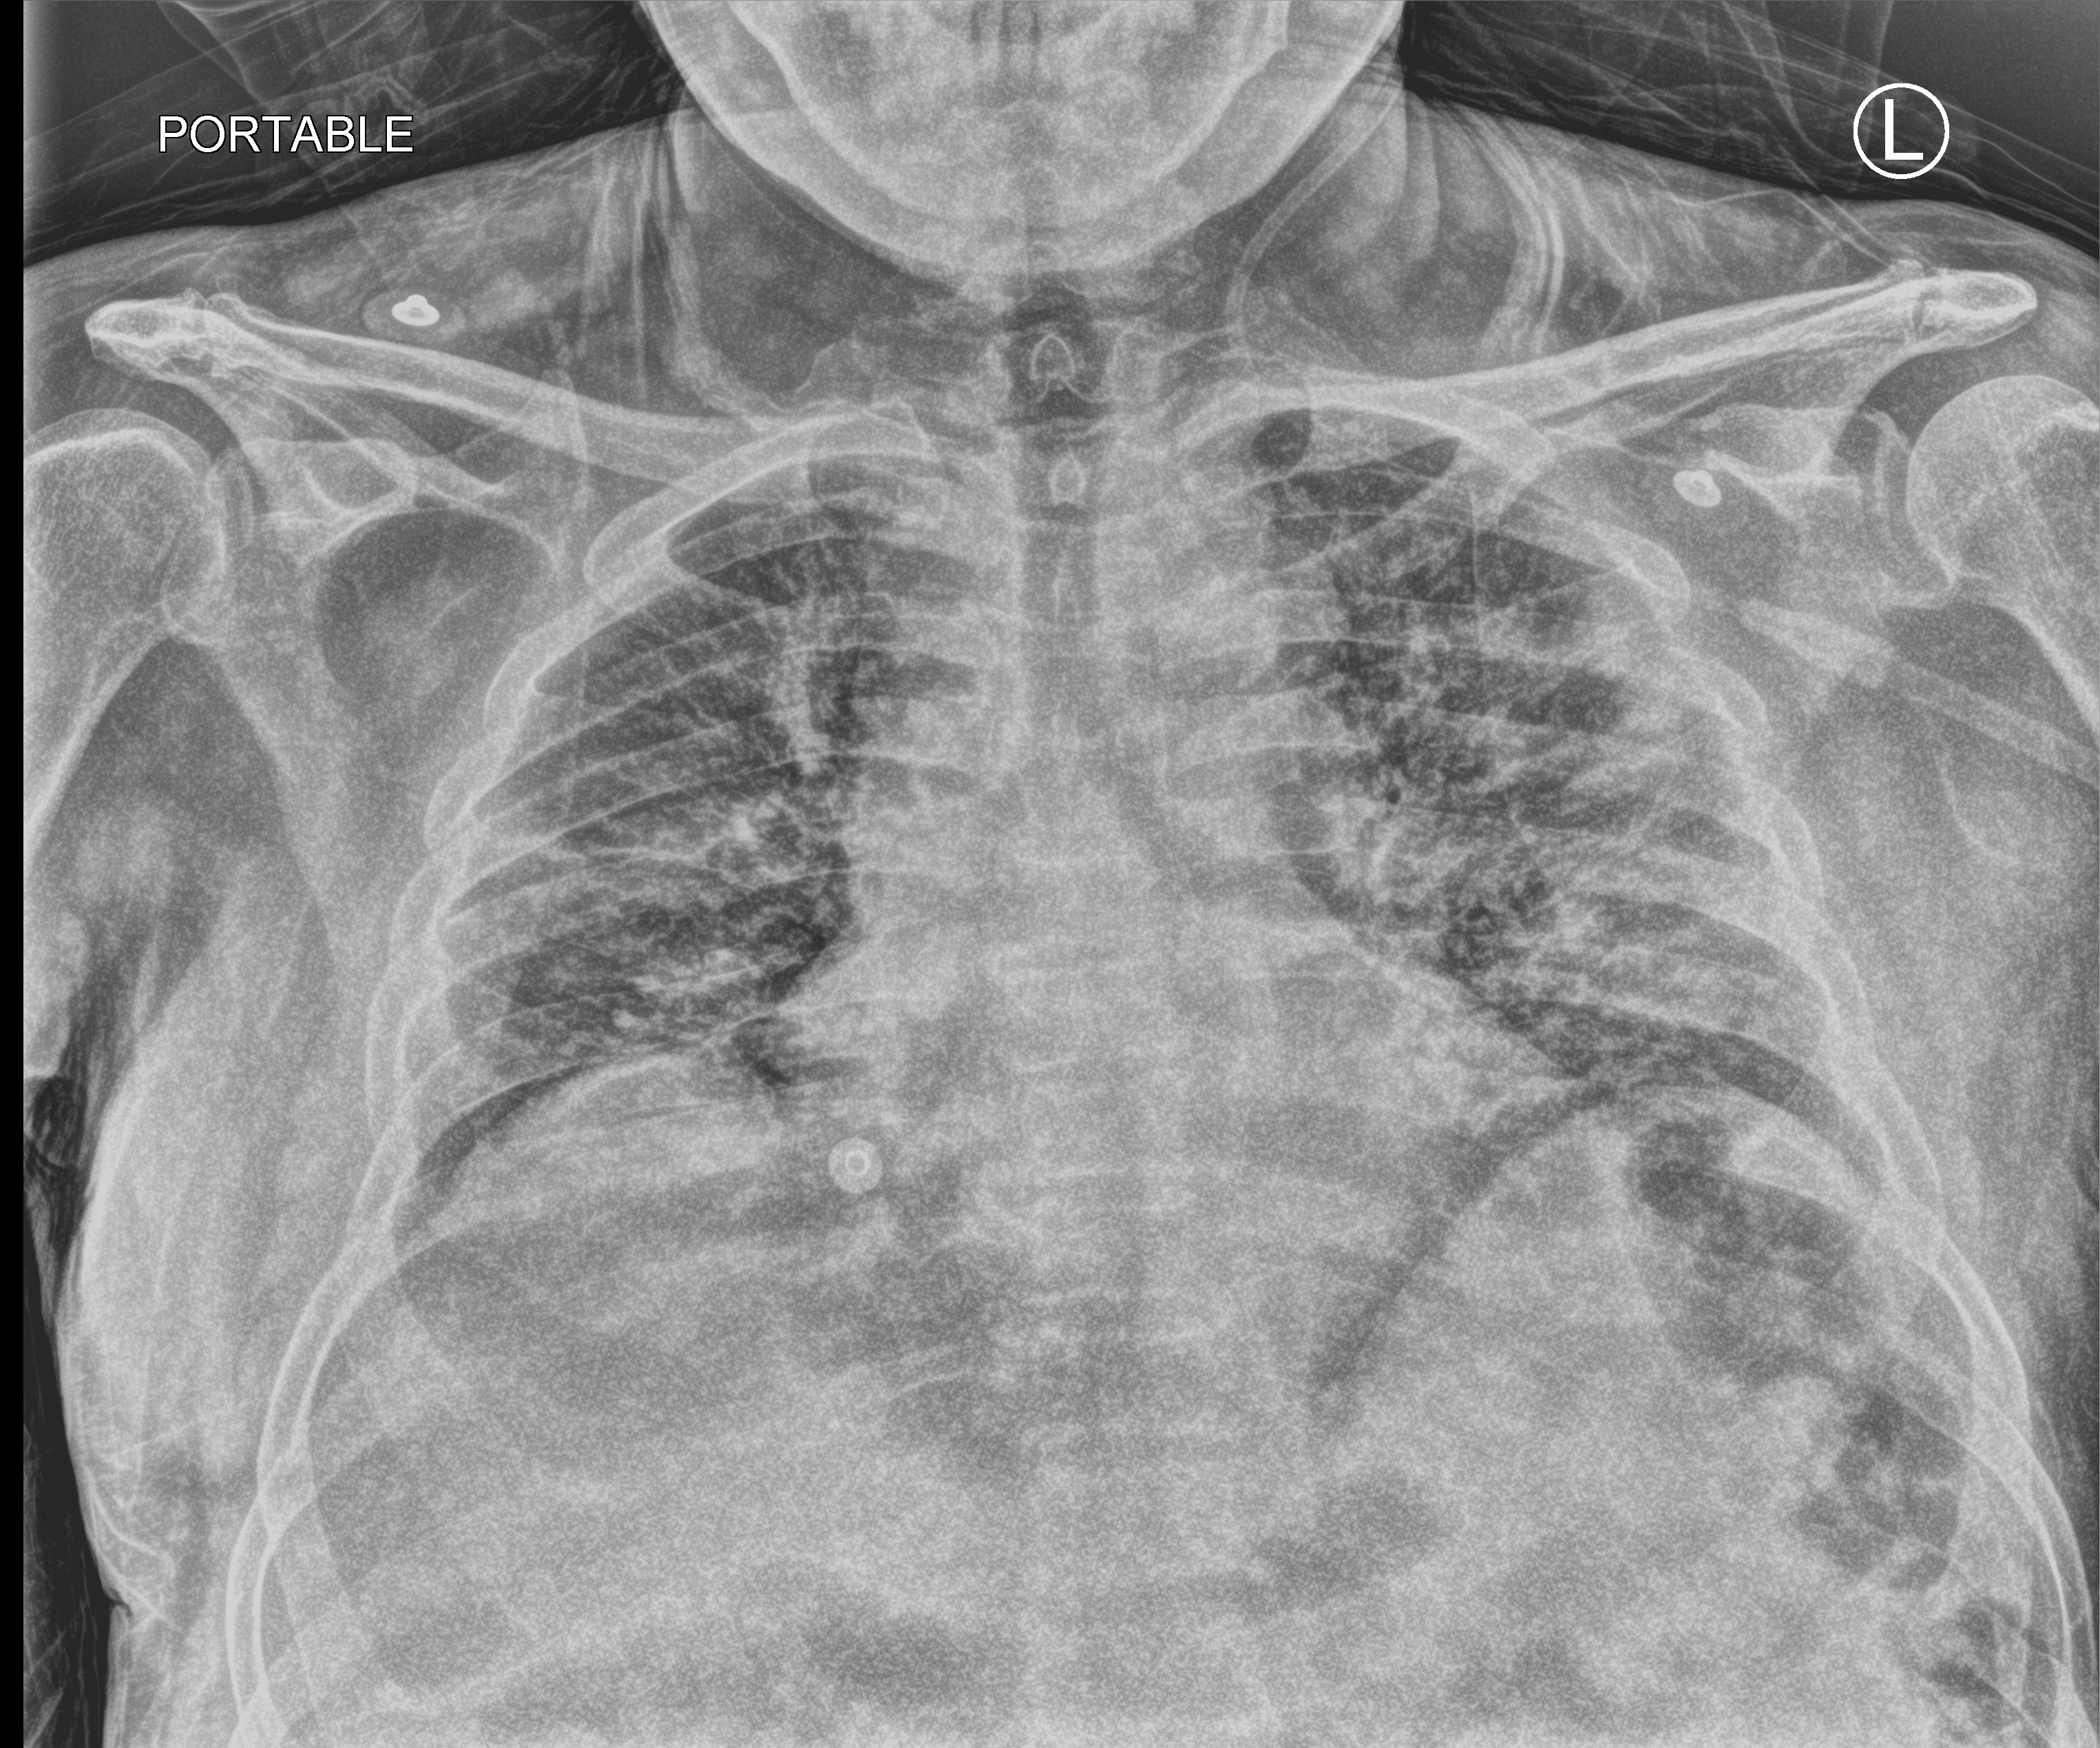
Chest X-ray (portable), anteroposterior (AP) projection. Male patient hospitalised with COVID-19, age 60–74 years.
Hospital-stay facts (about this admission, not read from this image; timing relative to this image not recorded):
- other chronic lung disease (admission record): no
- admitted to intensive care during this hospital stay: no